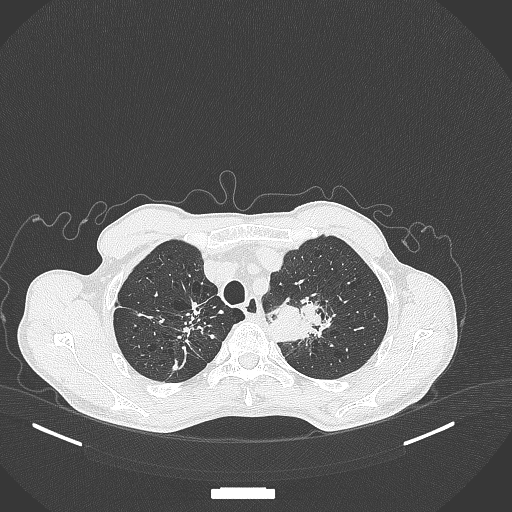
Chest CT, one axial slice. Slice 356 of 386 in the series (ordered by position). Reconstruction kernel B70f. 120 kVp. Lung window (W 1500 / L -600 HU). 1 mm slice thickness. 512 × 512 image matrix. Male patient, age 65 years. From the clinical record (not read from this slice): clinical TNM (as recorded): T2b N0 M0.
Annotated regions visible in this slice (bounding box drawn by a radiologist):
- lung tumour (recorded histology: adenocarcinoma): bounding box [x1, y1, x2, y2] px = [266, 286, 332, 351]